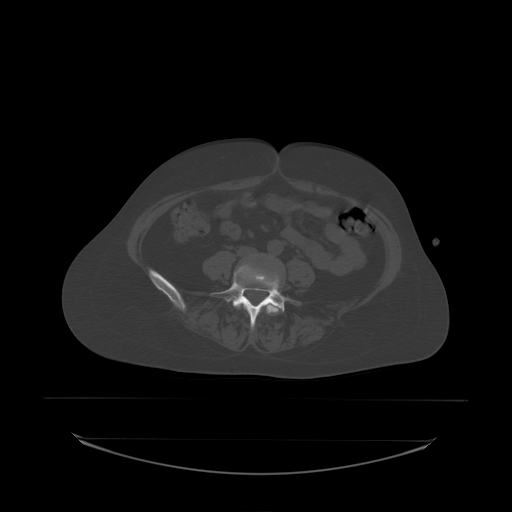
CT including the spine, one axial slice; position 42 of 242 along the scan axis; bone window (W 1800 / L 400 HU); 512 × 512 image matrix, field of view 500 × 500 mm. Female patient, age 53 years. From the clinical record (not read from this slice): primary cancer: lung; vertebrae with lytic lesions (as recorded): T7, L1.
Annotated regions visible in this slice (semi-automatically segmented with operator editing):
- L4 vertebra: bounding box [x1, y1, x2, y2] px = [266, 304, 279, 314]
- L5 vertebra: [214, 264, 302, 330]